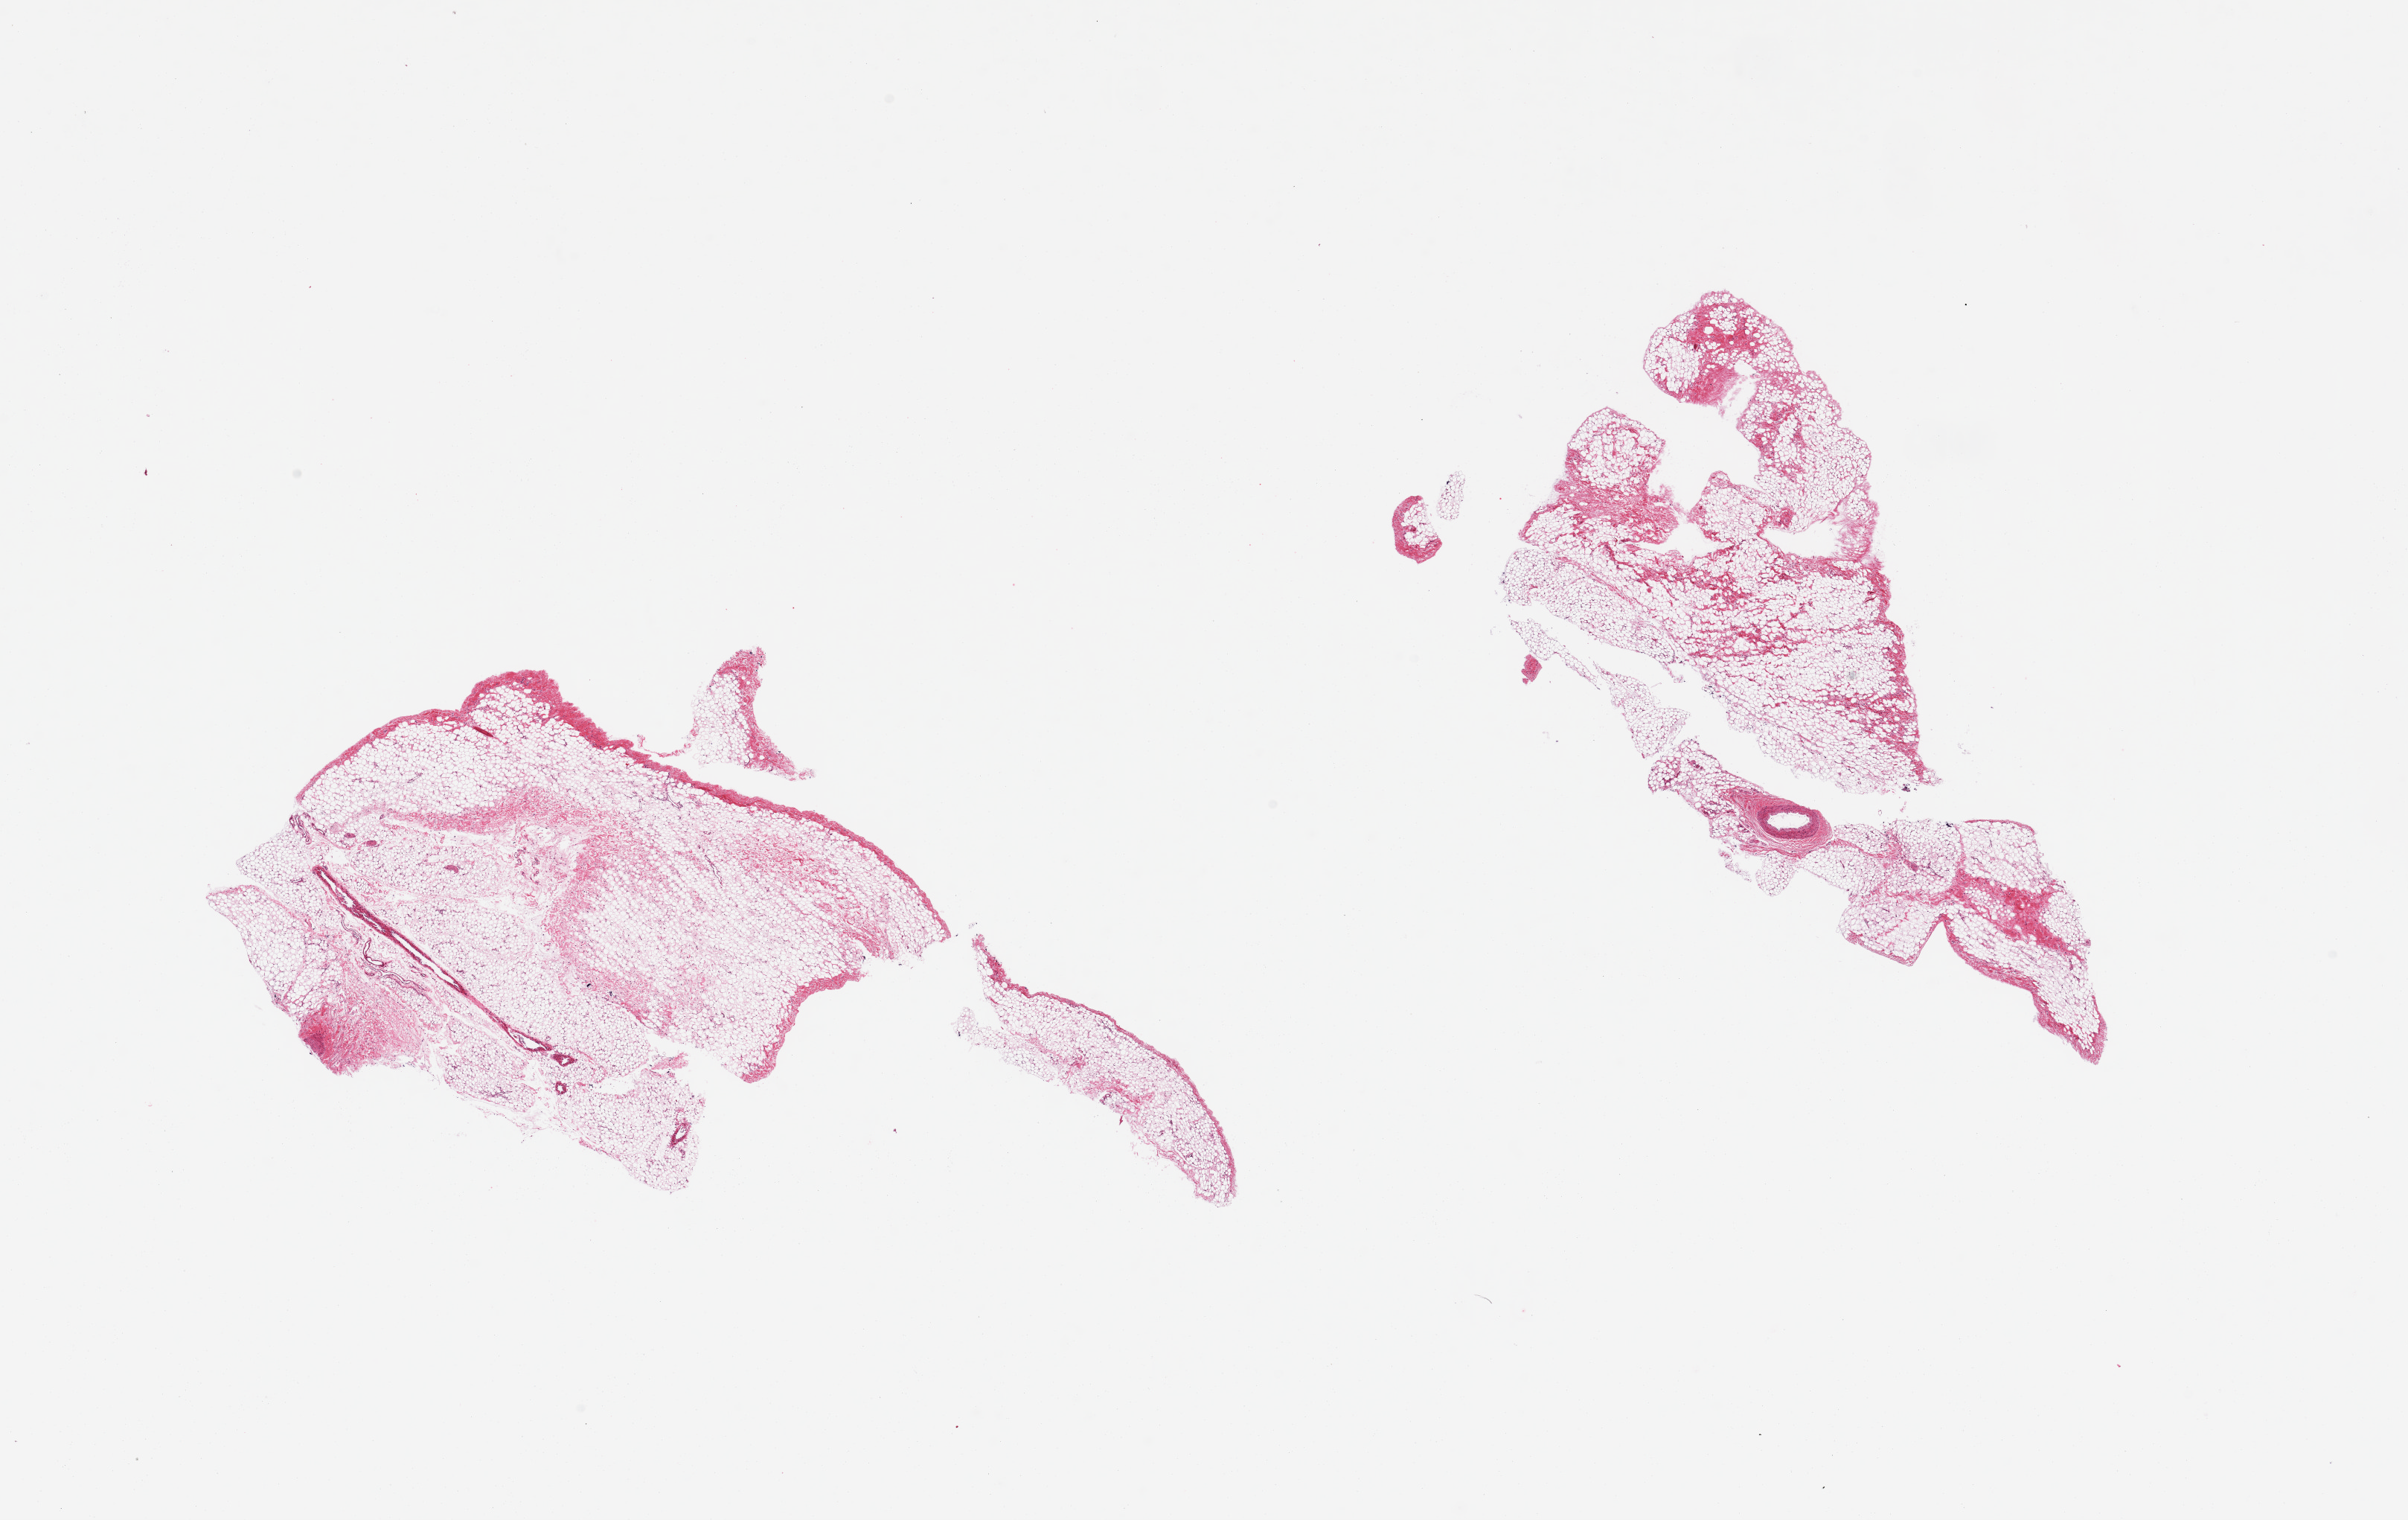
Hematoxylin and eosin (H&E) whole-slide image, a low-resolution overview of the entire scanned area, about 25.6 x 16.2 mm (from a 20x scan), PAXgene-fixed, paraffin-embedded tissue, target tissue: omentum, tissue donor sample.
Pathologist's review note for this sample: 2 pieces; adipose tissue and fibrovascular component.